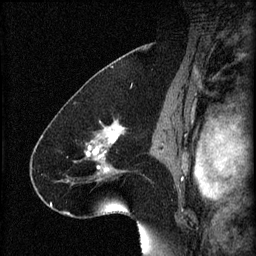
Breast MRI (dynamic contrast-enhanced), one sagittal slice. Slice 41 of 60 in the series (ordered by position). 3 images stored at this slice position (order not interpretable as contrast timing). 1.5 T. TE 4.2 ms, TR 8.2 ms. 2 mm slice thickness. 256 × 256 image matrix. Patient: female, 41 years.
Structures marked on this image (semi-automatically segmented with operator editing):
- analysis volume of interest (the breast-tissue region the enhancement analysis was run in; not a lesion): box from (x=72, y=120) to (x=132, y=187) px
- tumour enhancement mask (voxels above the 70 % enhancement threshold inside the analysis volume of interest): (x=86, y=122)–(x=123, y=175)